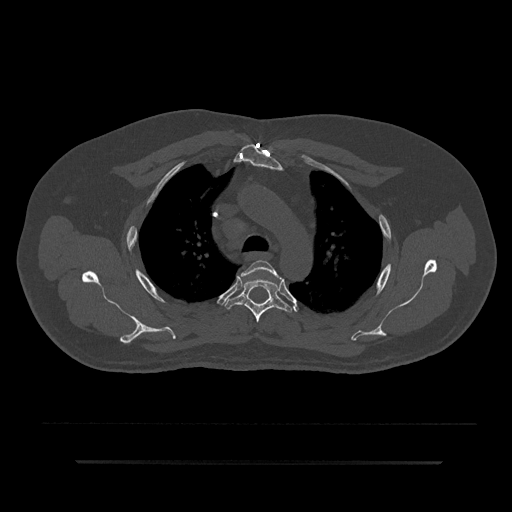
CT including the spine, one axial slice; slice 625 of 797 in the series (ordered by position); reconstruction kernel Br40s/3; 120 kVp; bone window (W 1800 / L 400 HU); 512 × 512 image matrix. Male patient, age 59 years. Case-level facts recorded for this patient, not image findings: primary cancer: bile ducts; vertebrae with lytic lesions (as recorded): T10.
Structures marked on this image (semi-automatic segmentation, software-assisted and operator-edited):
- T3 vertebra: bounding box [x1, y1, x2, y2] px = [241, 260, 282, 281]
- T4 vertebra: [224, 272, 292, 323]